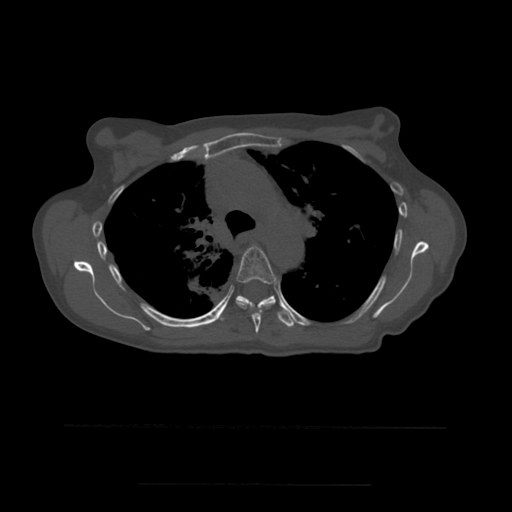
CT including the spine, one axial slice; slice 387 of 544 in the series (ordered by position); bone window (W 1800 / L 400 HU); 1.25 mm slice thickness; 512 × 512 image matrix, field of view 350 × 350 mm. Patient age 58 years. From the clinical record (not read from this slice): primary cancer: lung.
Annotated regions visible in this slice (semi-automatic segmentation, software-assisted and operator-edited):
- T5 vertebra: bounding box [x1, y1, x2, y2] px = [236, 247, 277, 334]
- T6 vertebra: [220, 295, 296, 327]